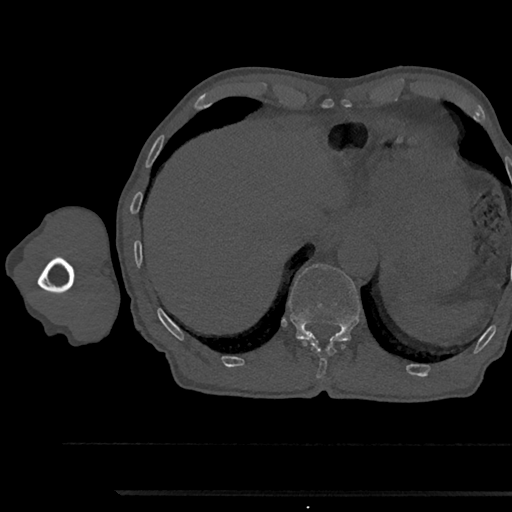
CT including the spine, one axial slice; slice 748 of 797 in the series (ordered by position); 120 kVp; bone window (W 1800 / L 400 HU); 512 × 512 image matrix. Patient: male, 79 years. From the clinical record (not read from this slice): primary cancer: prostate.
Annotated regions visible in this slice (semi-automatic segmentation, software-assisted and operator-edited):
- T11 vertebra: box from (x=304, y=340) to (x=335, y=378) px
- T12 vertebra: (x=289, y=264)–(x=360, y=342)